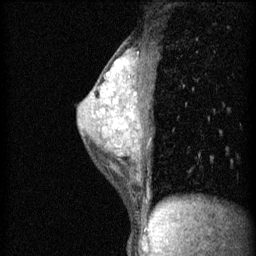
Breast MRI (dynamic contrast-enhanced), one sagittal slice; position 37 of 60 along the scan axis; 3 images stored at this slice position (order not interpretable as contrast timing); 1.5 T; TE 4.2 ms, TR 11 ms; 2 mm slice thickness; 256 × 256 image matrix. Female patient, age 40 years.
Structures marked on this image (semi-automatic segmentation, software-assisted and operator-edited):
- analysis volume of interest (the breast-tissue region the enhancement analysis was run in; not a lesion): bounding box [x1, y1, x2, y2] px = [79, 50, 153, 189]
- tumour enhancement mask (voxels above the 70 % enhancement threshold inside the analysis volume of interest): [116, 116, 135, 129]